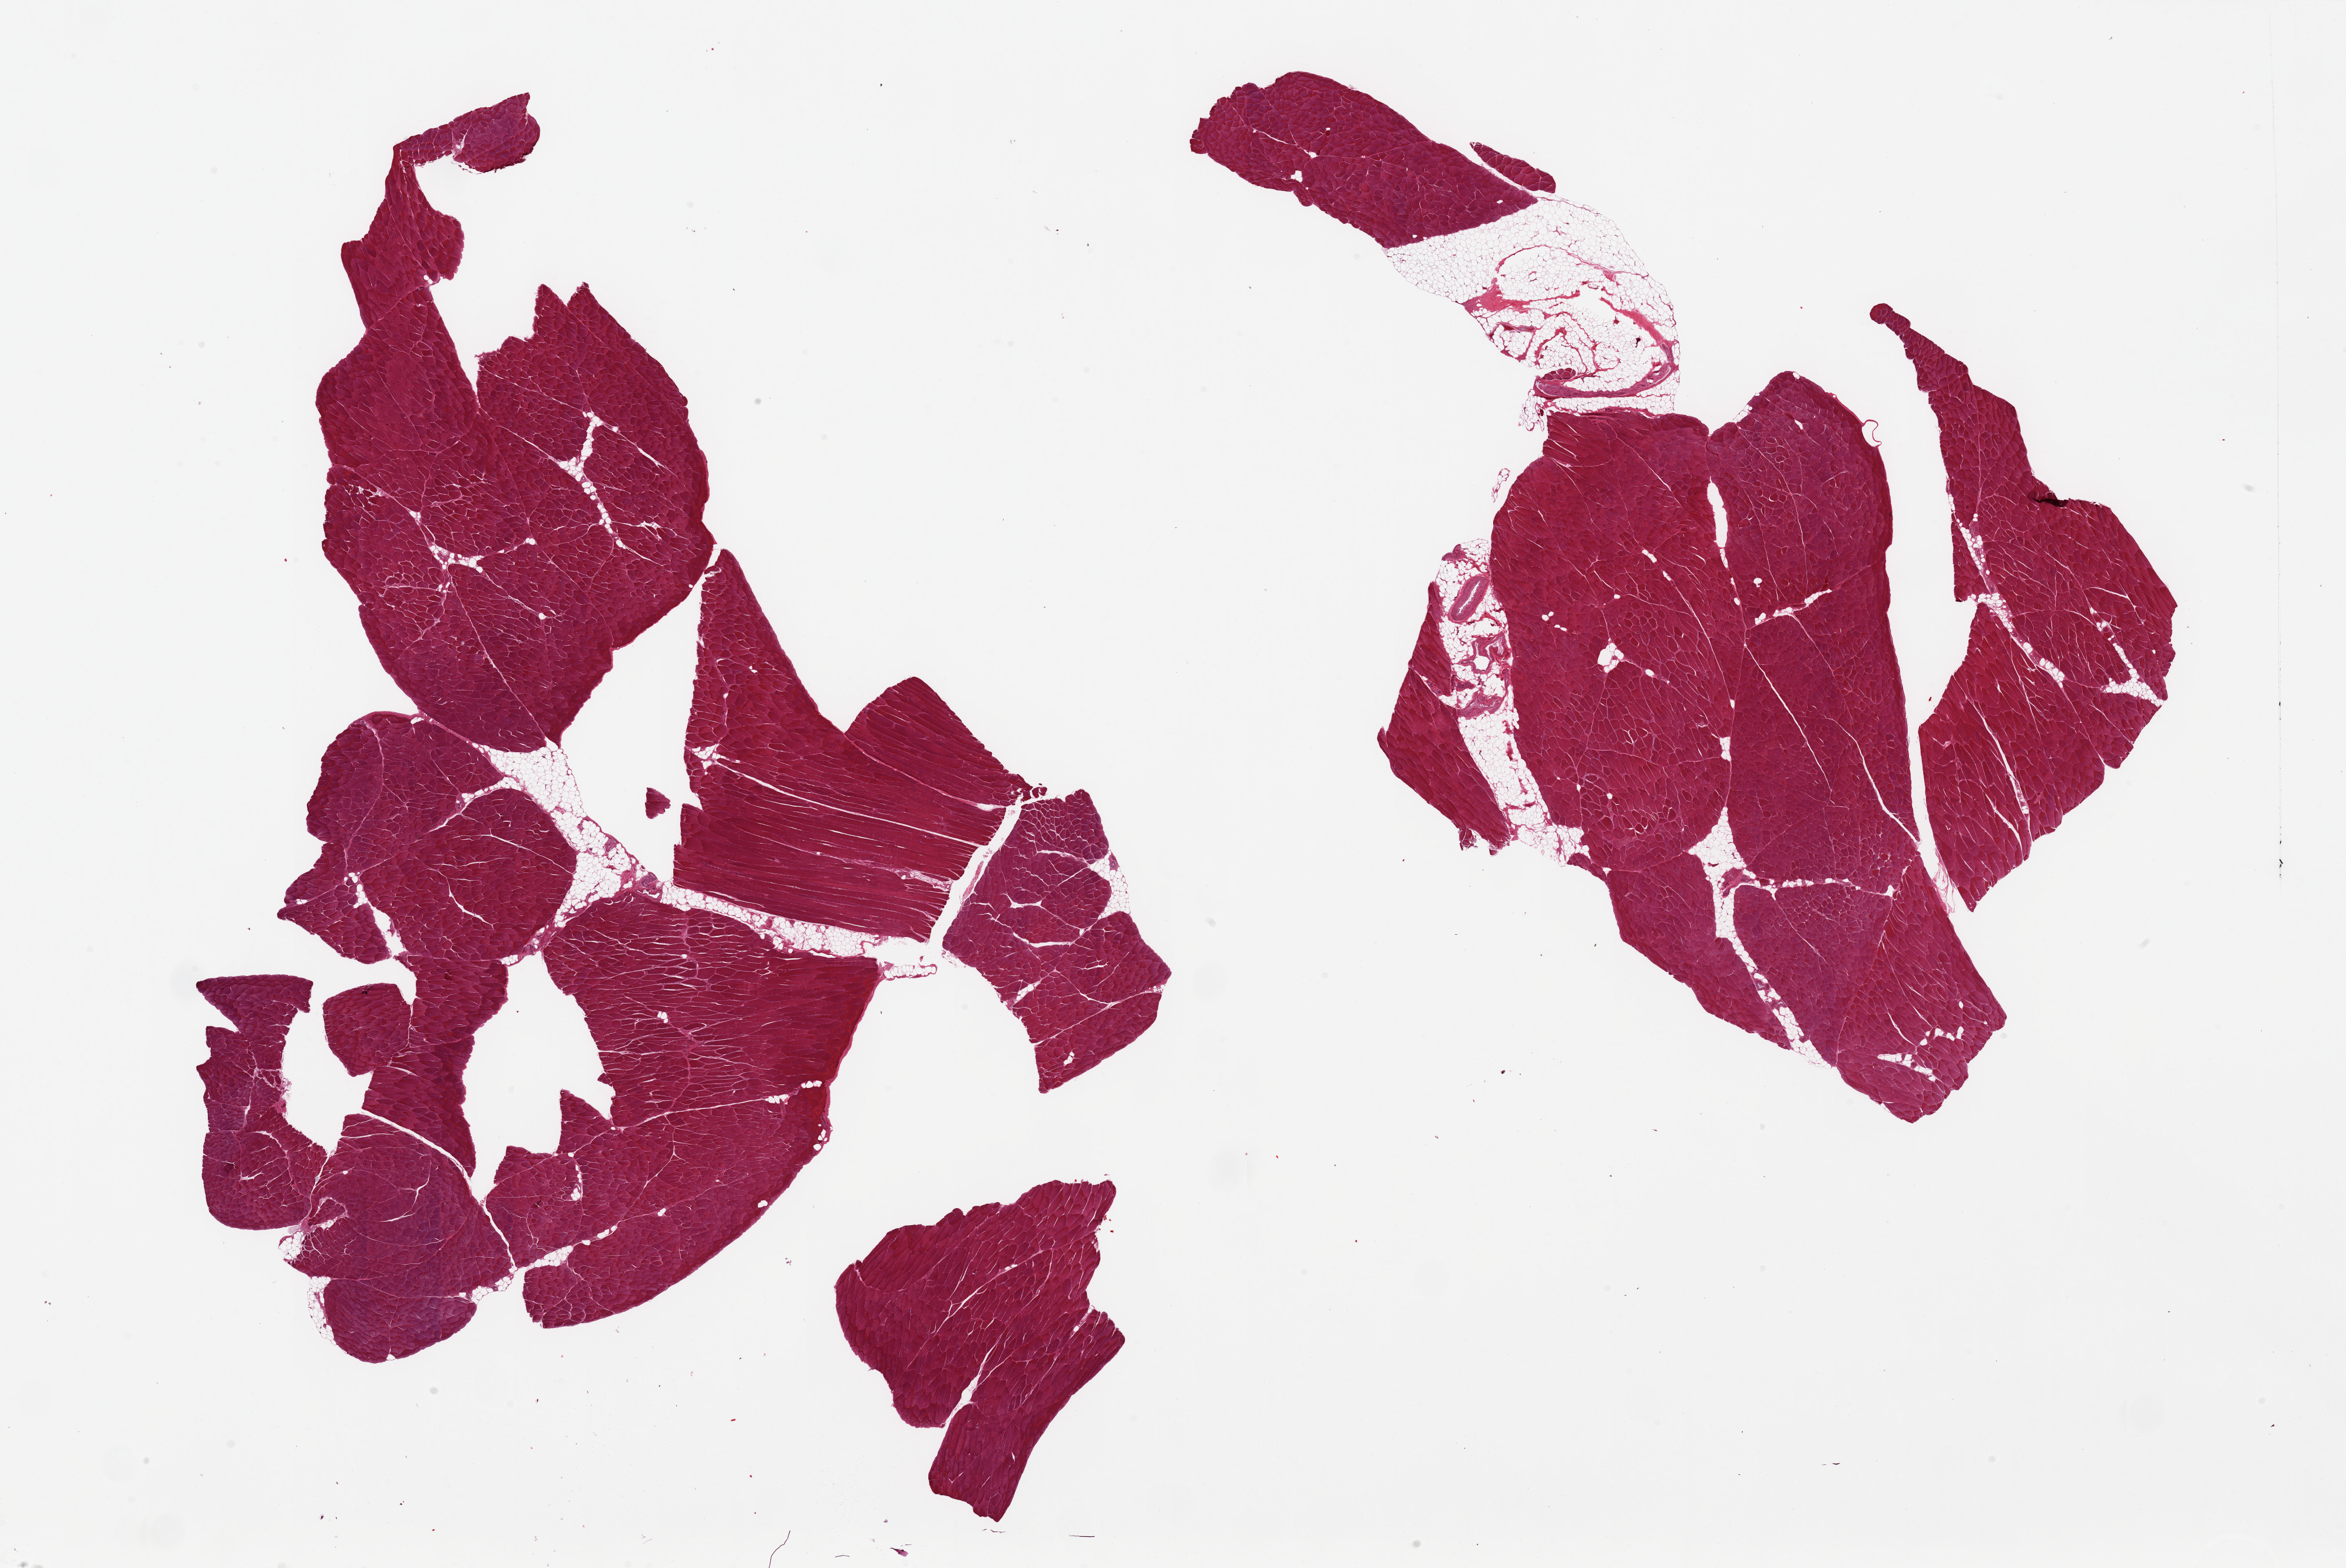
Digitized H&E-stained section, whole scanned area (about 31.5 x 21.1 mm, from a 20x scan) shown as a low-resolution overview; PAXgene-fixed paraffin-embedded (PFPE) section; target tissue: skeletal muscle; tissue donor sample.
Reviewer comment on this tissue sample: 2 pieces; minimal interstitial fat.